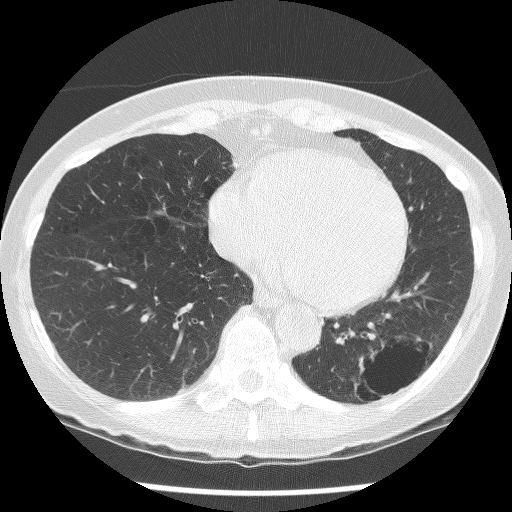
Chest CT (low-dose screening protocol), one axial image, second screening round (one year after baseline), lung window (W 1500 / L -600 HU), 2.5 mm slice thickness, lung (sharp) reconstruction kernel (BONE), slice 89 of 136 in the series. Female, age 61 years at enrolment. Current smoker at enrolment.
Expert reader's lesion annotation, bounding box <333,328,437,417> (left, top, right, bottom; pixels). The screening reader recorded 2 non-calcified nodules or masses ≥4 mm on this exam (left lower lobe, left lower lobe); which of them this box marks is not recorded. Official screen result: positive, no significant change: stable abnormalities potentially related to lung cancer, unchanged since the prior screening exam.